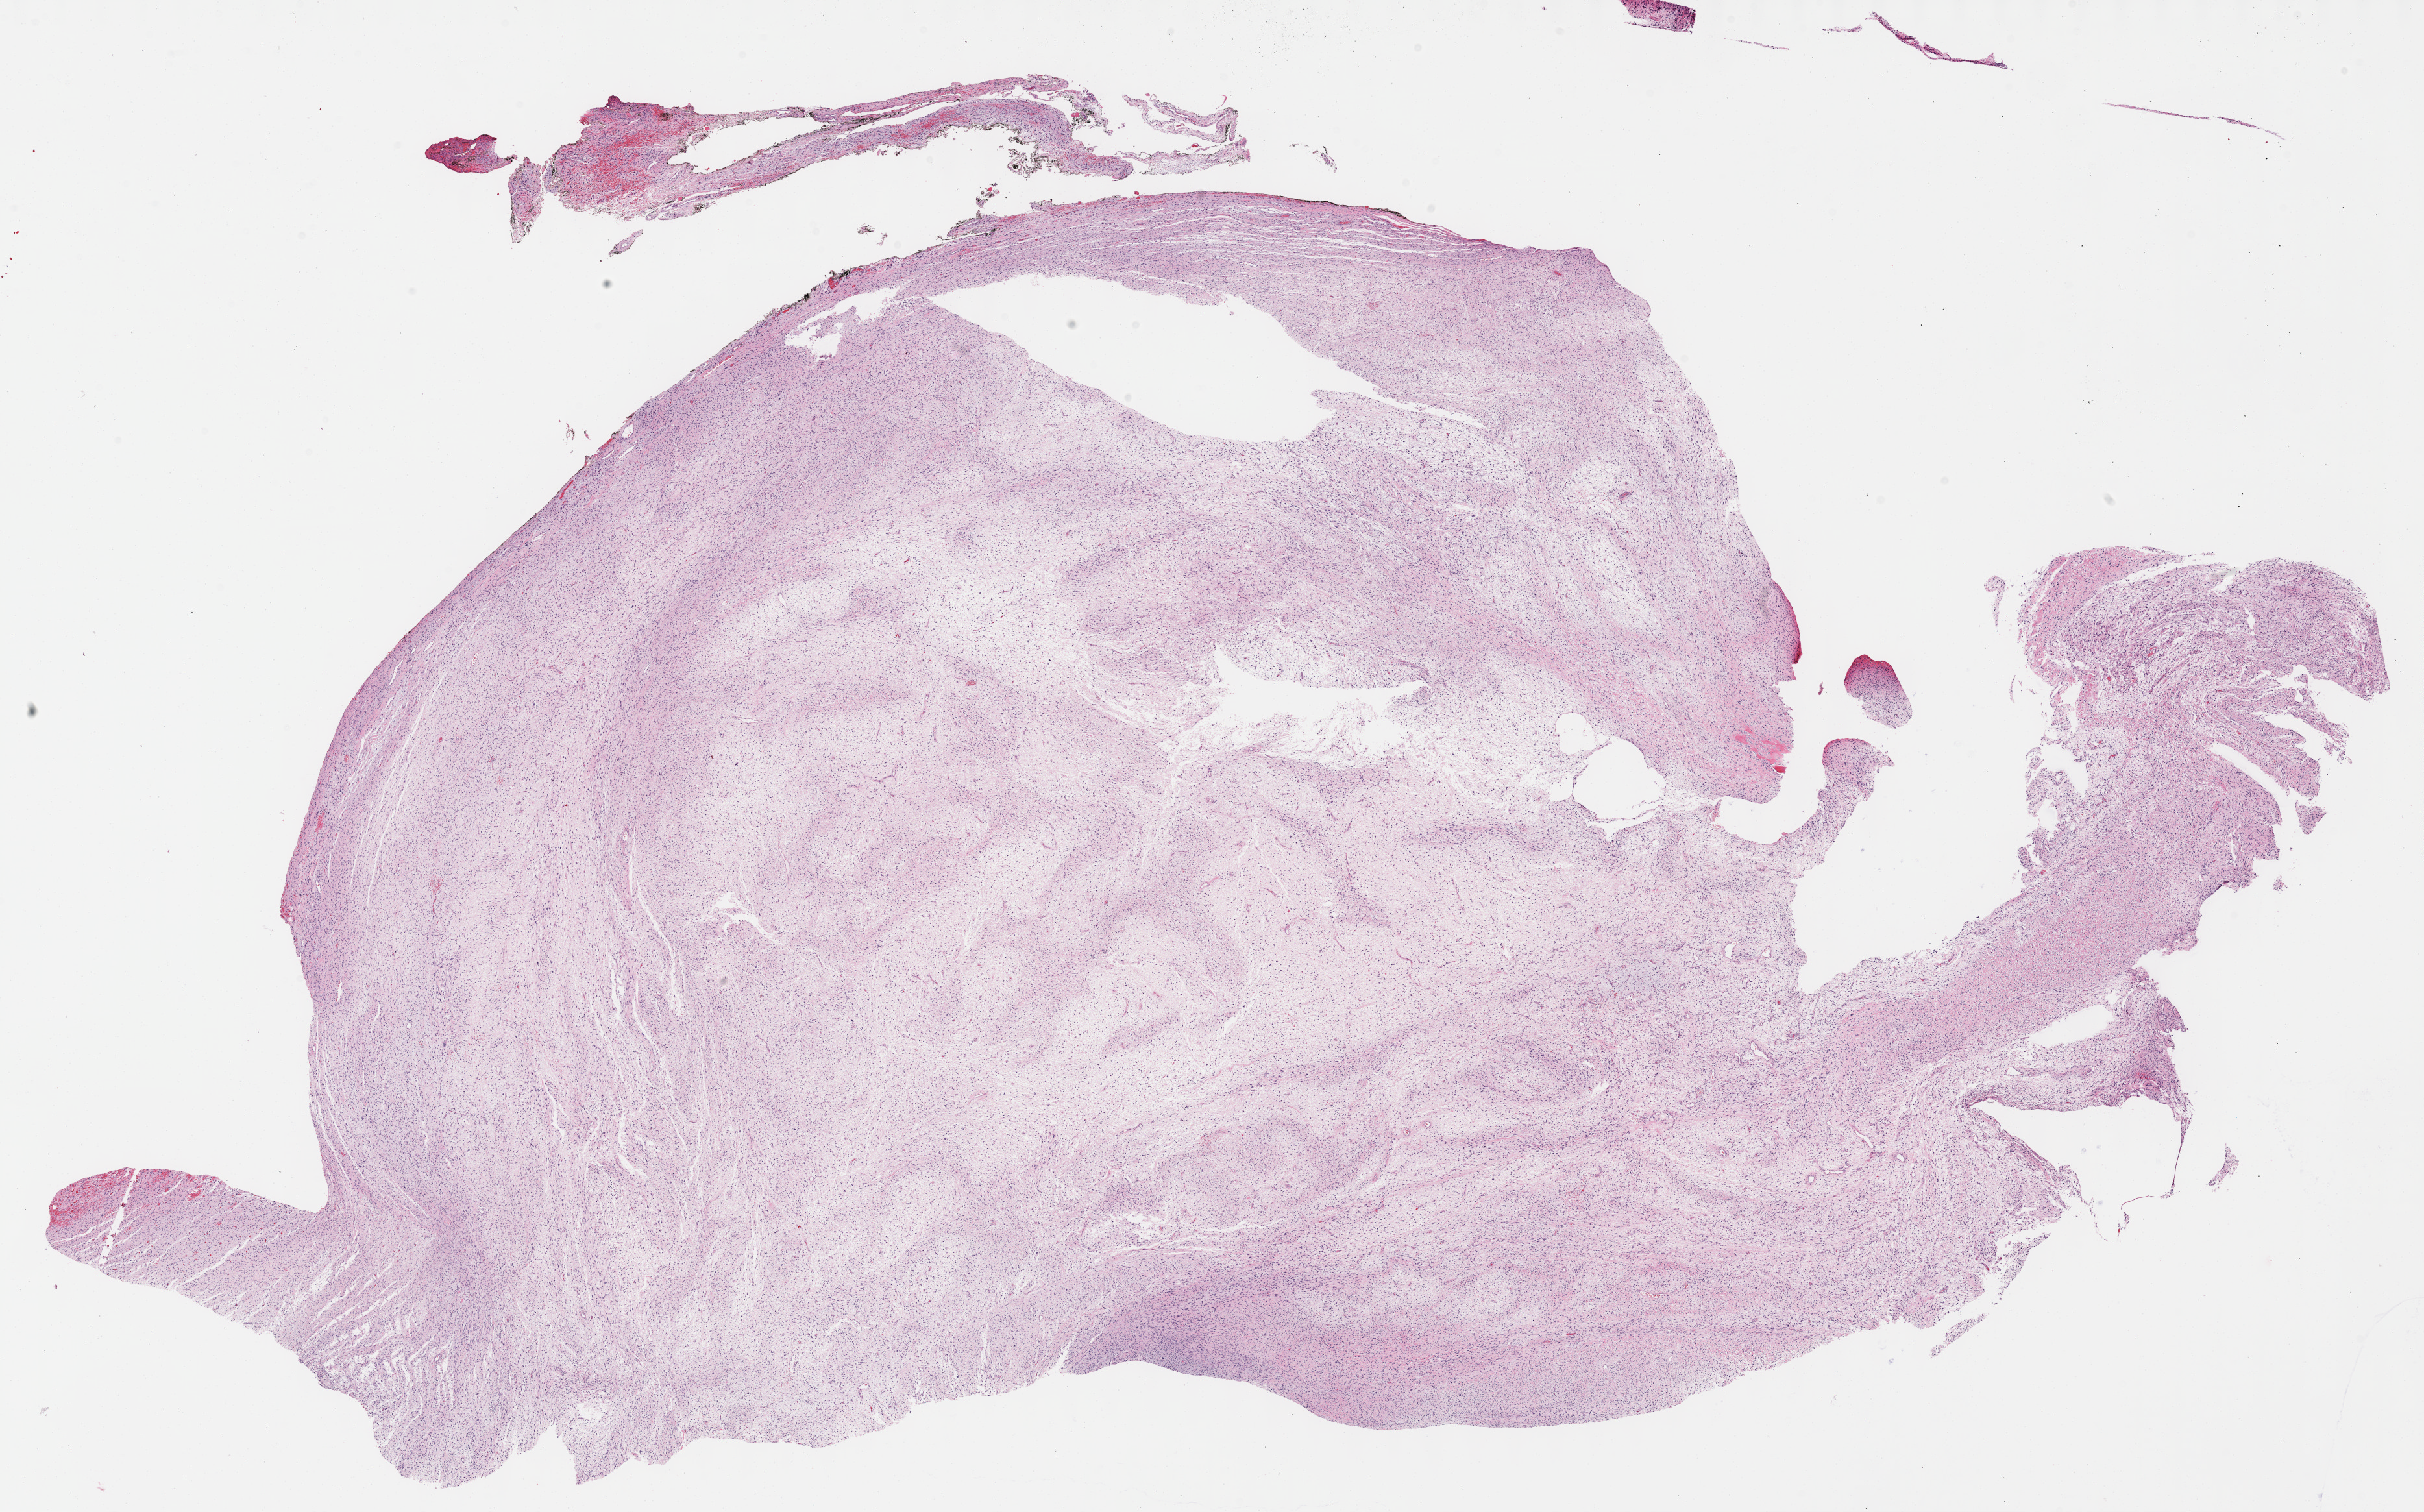
Hematoxylin and eosin (H&E) stained whole-slide image, shown as a low-resolution overview of the whole scanned area (about 30.2 x 18.8 mm, slide scanned at 40x). Formalin-fixed paraffin-embedded (FFPE) diagnostic section. Retroperitoneum and peritoneum, primary tumour sample. Male patient; age at initial diagnosis 72 years.
* pathologic diagnosis: Sarcoma, NOS